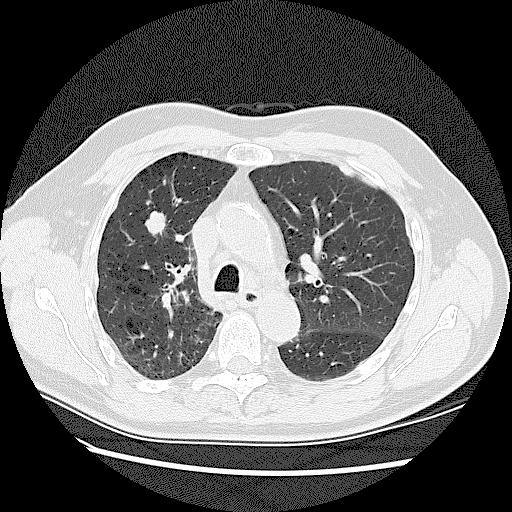
Low-dose screening chest CT, axial slice; baseline annual screen; lung window (W 1500 / L -600 HU); 2.5 mm slice thickness; slice 43 of 128 in the series. Male participant, aged 72 years at enrolment.
- Lesion marked by an expert reader, bounding box <133,203,182,241> (left, top, right, bottom; pixels).
- The screening reader recorded 2 non-calcified nodules or masses ≥4 mm on this exam (right upper lobe, right upper lobe); which of them this box marks is not recorded.
- Lung cancer was diagnosed 42 days after this screen: adenocarcinoma, NOS, right upper lobe, stage IV (AJCC 6th edition), 45 mm at pathology.